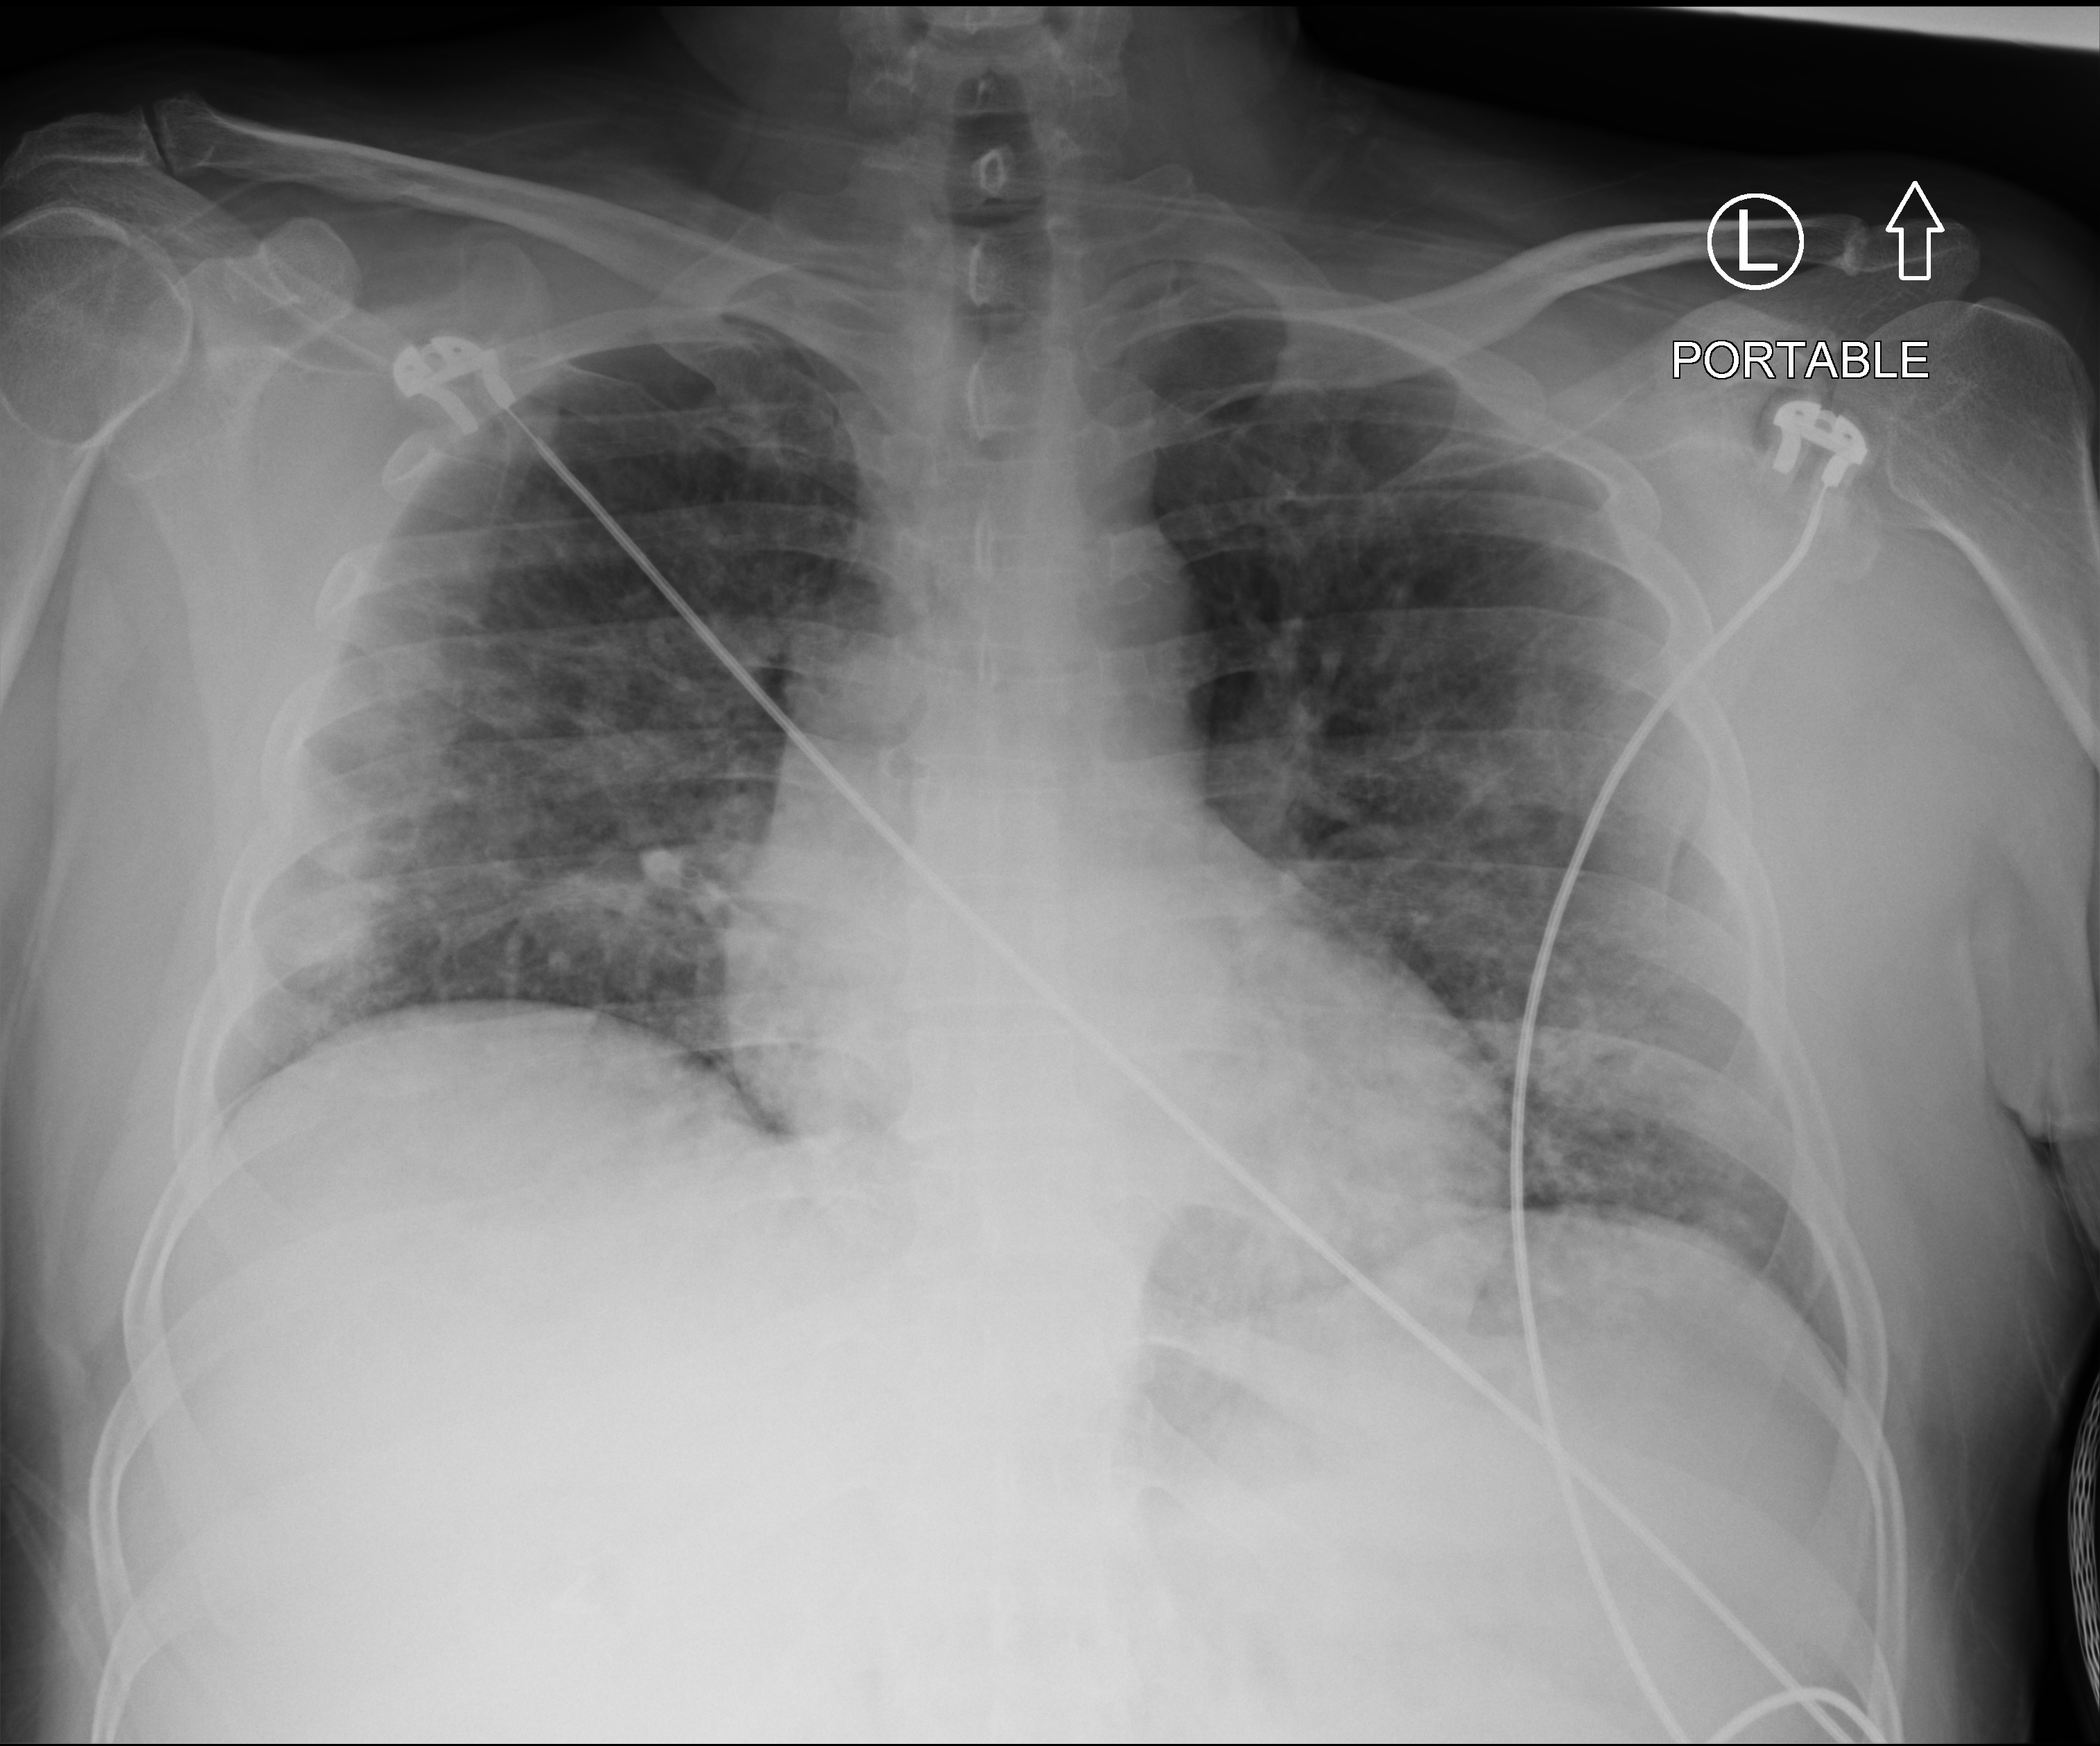
Chest X-ray (portable), anteroposterior (AP) projection. Patient hospitalised with COVID-19; male, aged 18–59 years.
Hospital-stay facts (about this admission, not read from this image; timing relative to this image not recorded):
- mechanically ventilated during this hospital stay: no
- admitted to intensive care during this hospital stay: no
- chronic kidney disease (admission record): no